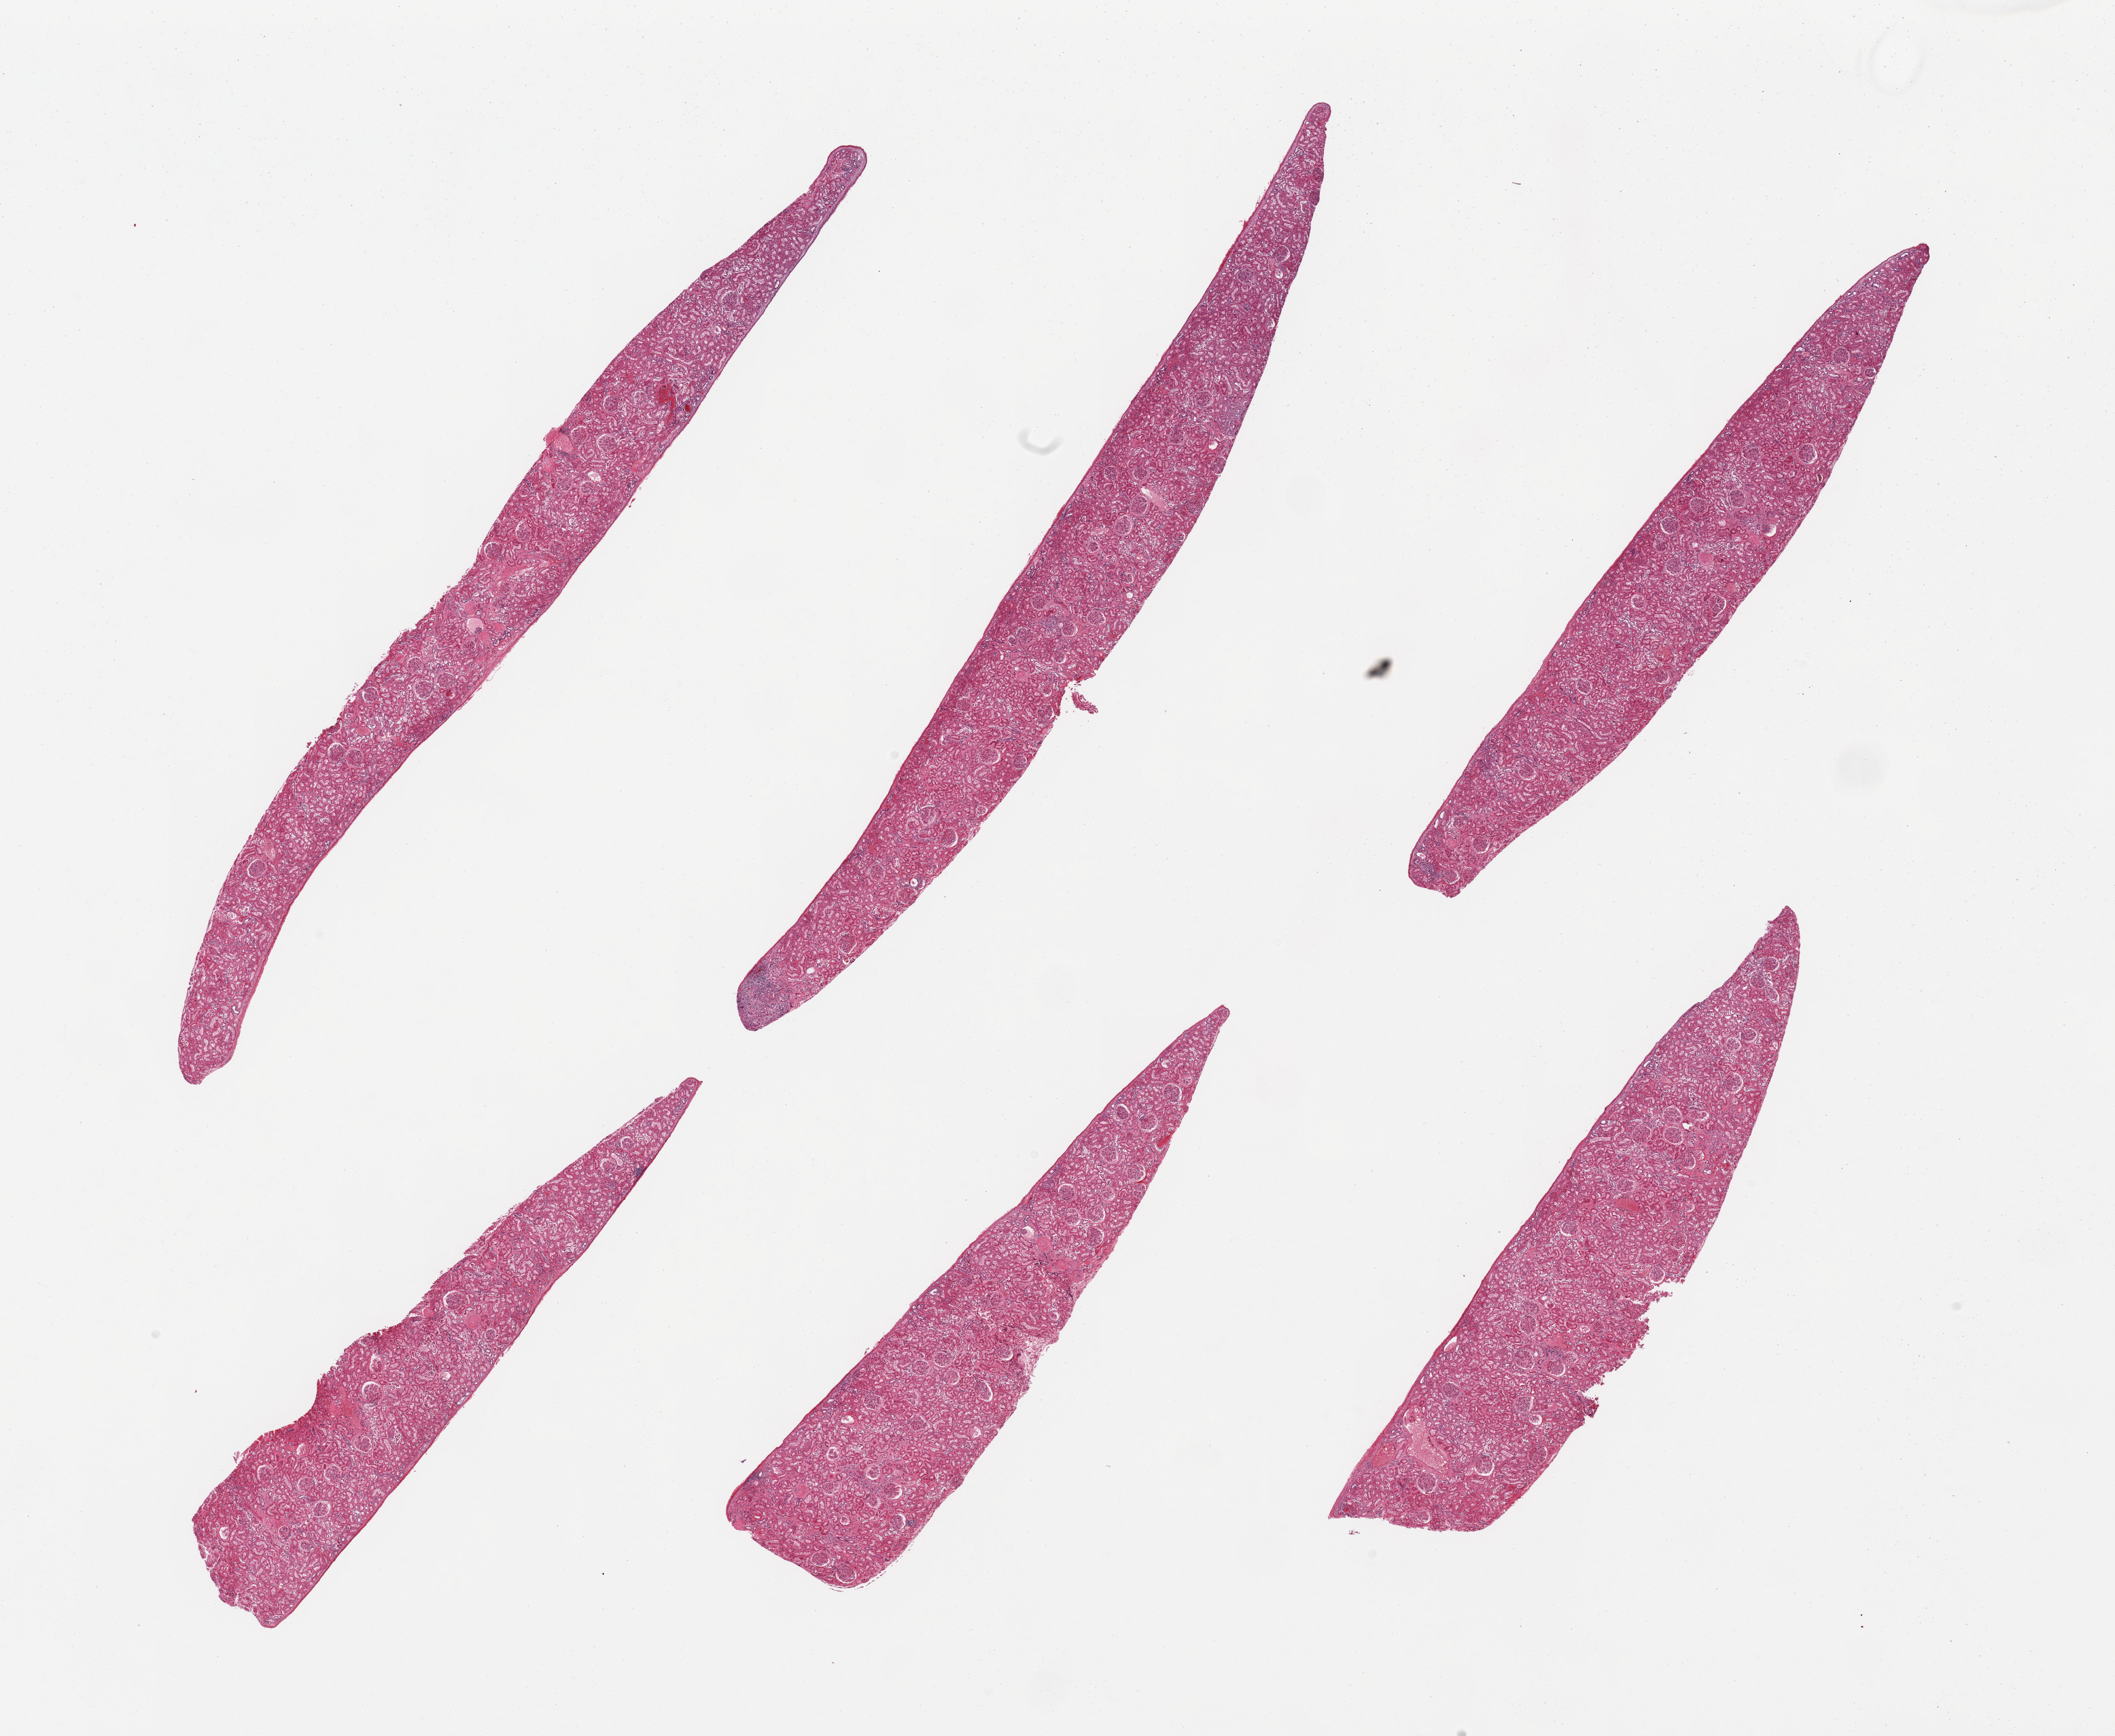
Digitized H&E-stained section — a low-resolution overview of the entire scanned area, about 24.6 x 20.2 mm, PAXgene-fixed paraffin-embedded (PFPE) section, target tissue: renal cortex, donor tissue sample. Donor sex: male.
* reviewer comment on this tissue sample: 6 pieces; occasional sclerosed glomeruli and small lymphoid collections